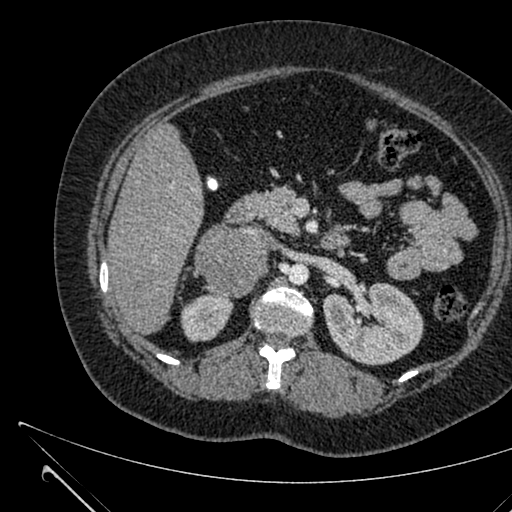
Contrast-enhanced abdominal CT, one axial slice. Slice 375 of 731 in the series (ordered by position). Intravenous contrast given. Soft-tissue window (W 400 / L 40 HU). 512 × 512 image matrix, field of view 376 × 376 mm. Female patient, age 36 years. From the clinical record (not read from this slice): diagnosis: adrenocortical carcinoma; tumour side: right adrenal; tumour size at pathology: 10 cm; Ki-67 index: 20 %; stage (as recorded): 4.
Structures marked on this image (semi-automatically segmented with operator editing):
- mass: box from (x=194, y=225) to (x=267, y=297) px